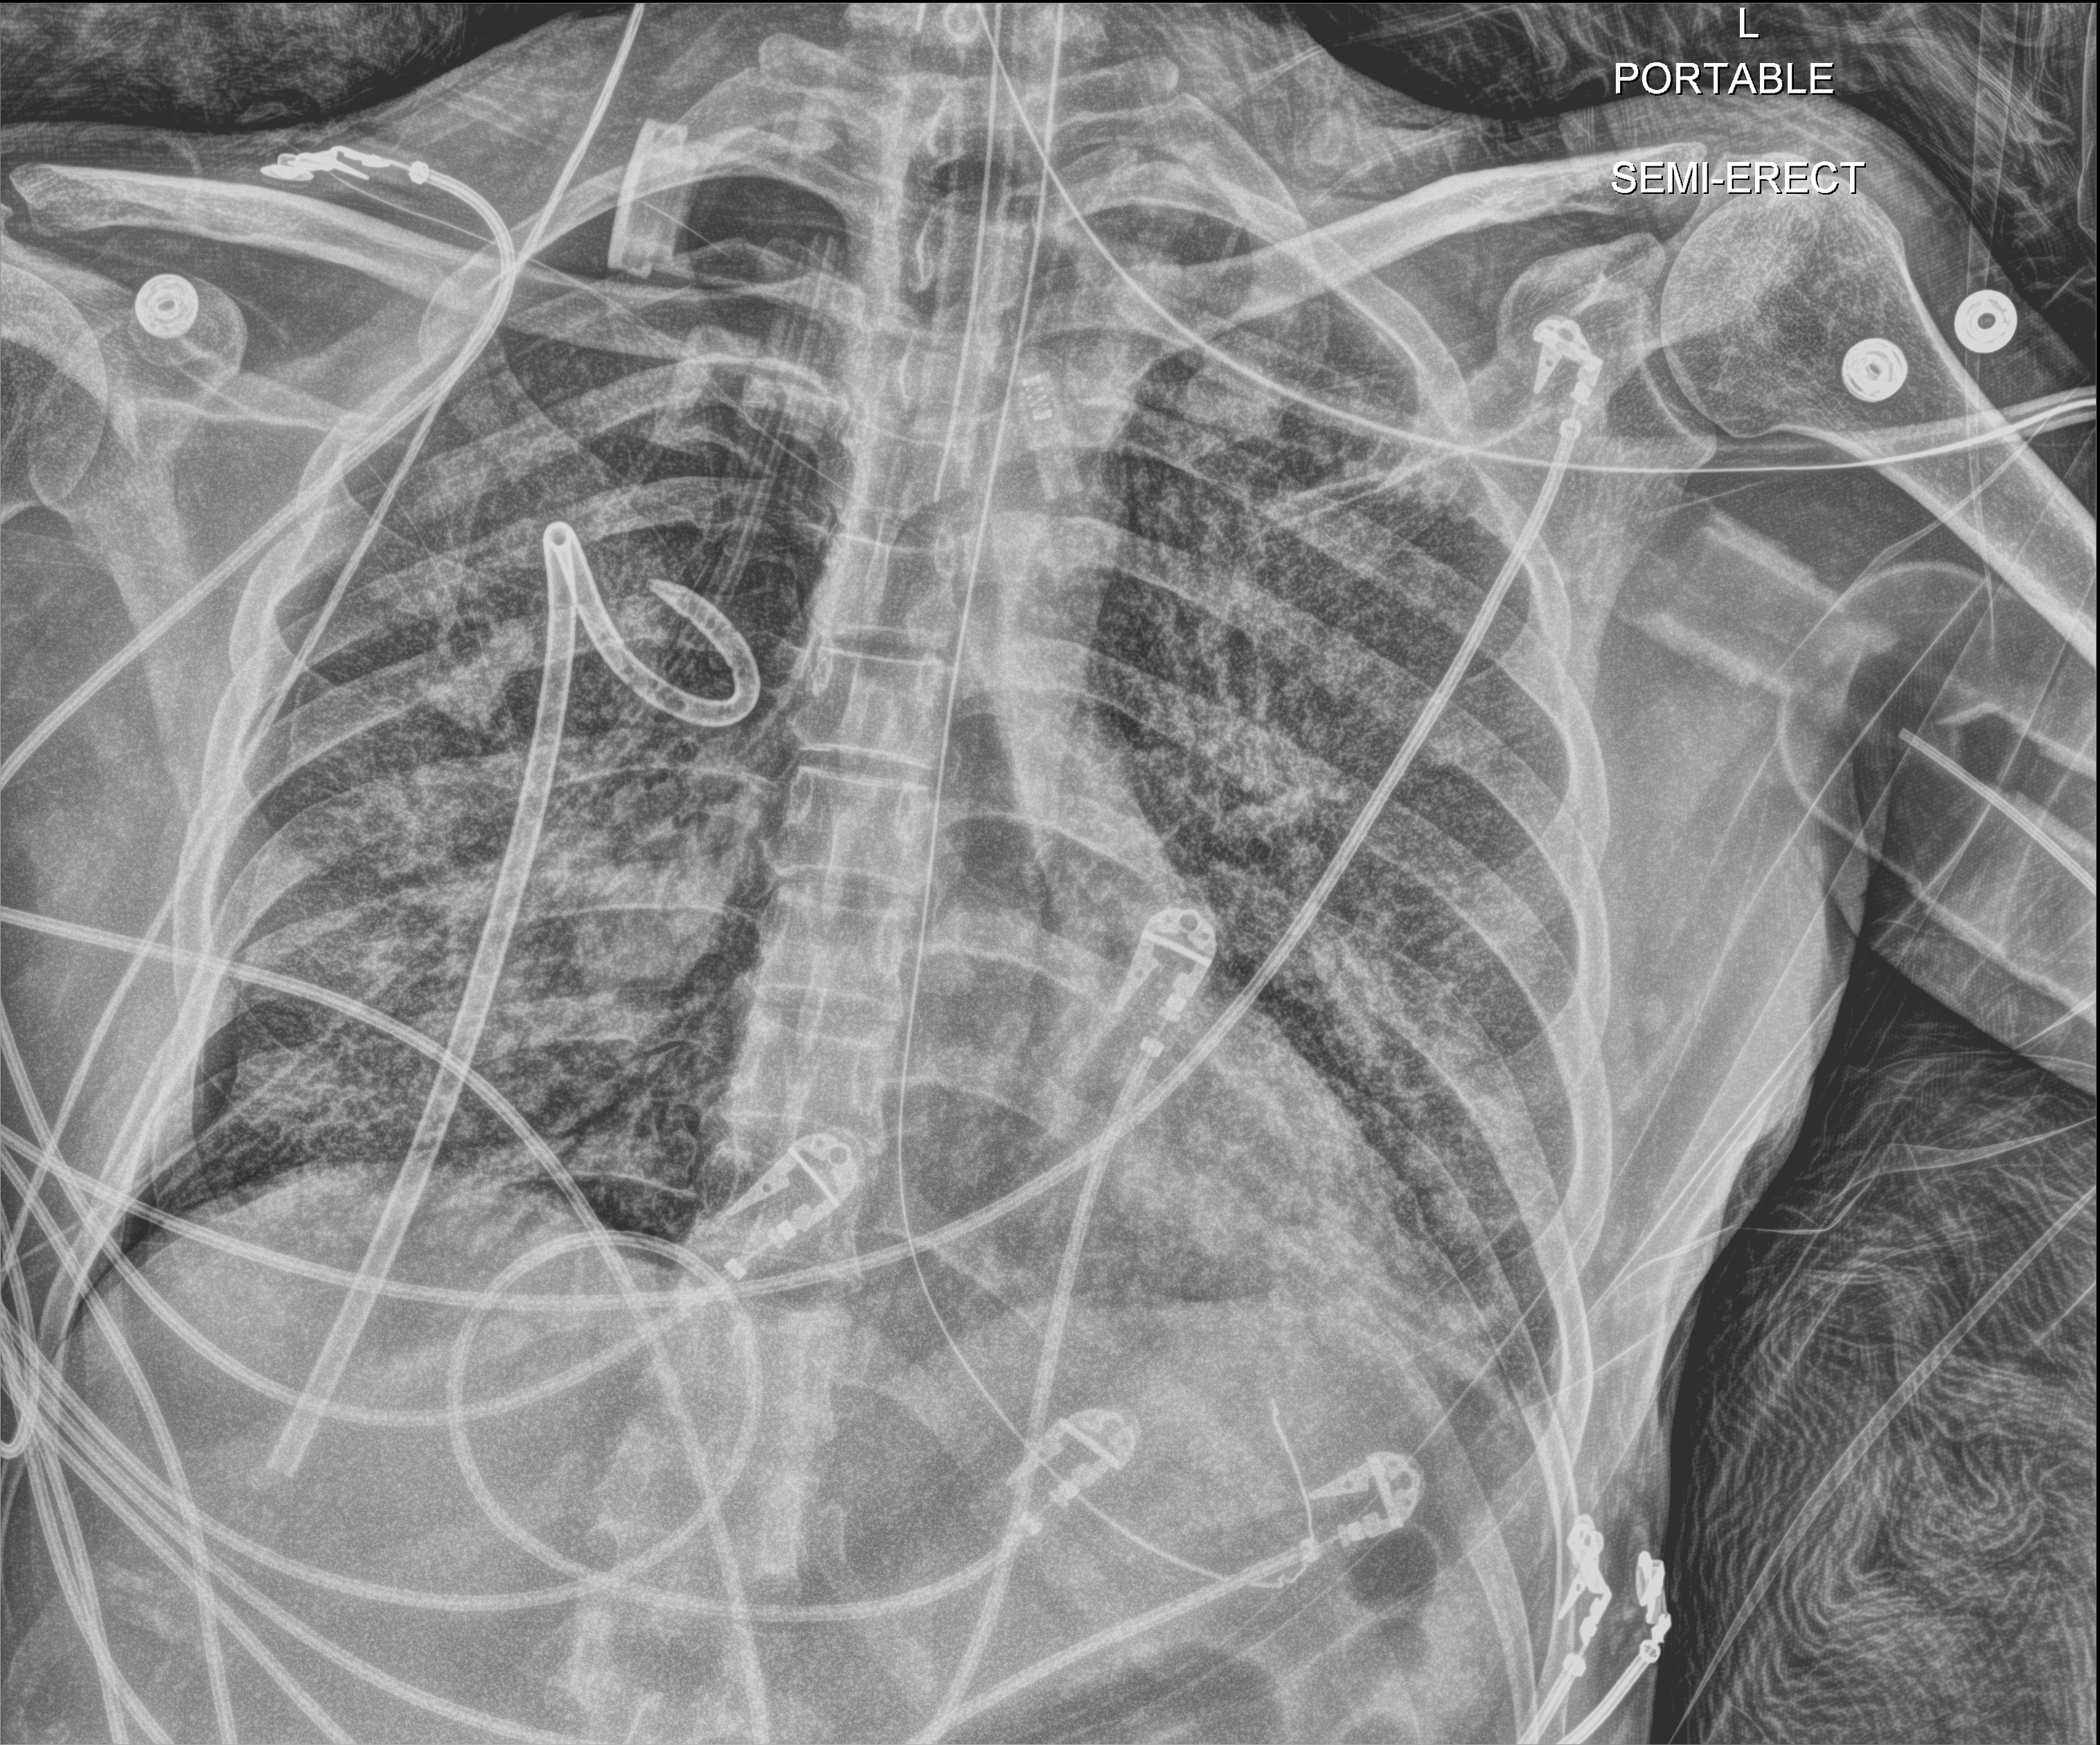
Chest radiograph (digital radiography), anteroposterior (AP) projection. Patient hospitalised with COVID-19, aged 18–59 years.
From the hospital-stay record, not from the radiograph (when in the stay this image was taken is not recorded): chronic kidney disease (admission record): no; mechanically ventilated during this hospital stay: yes.